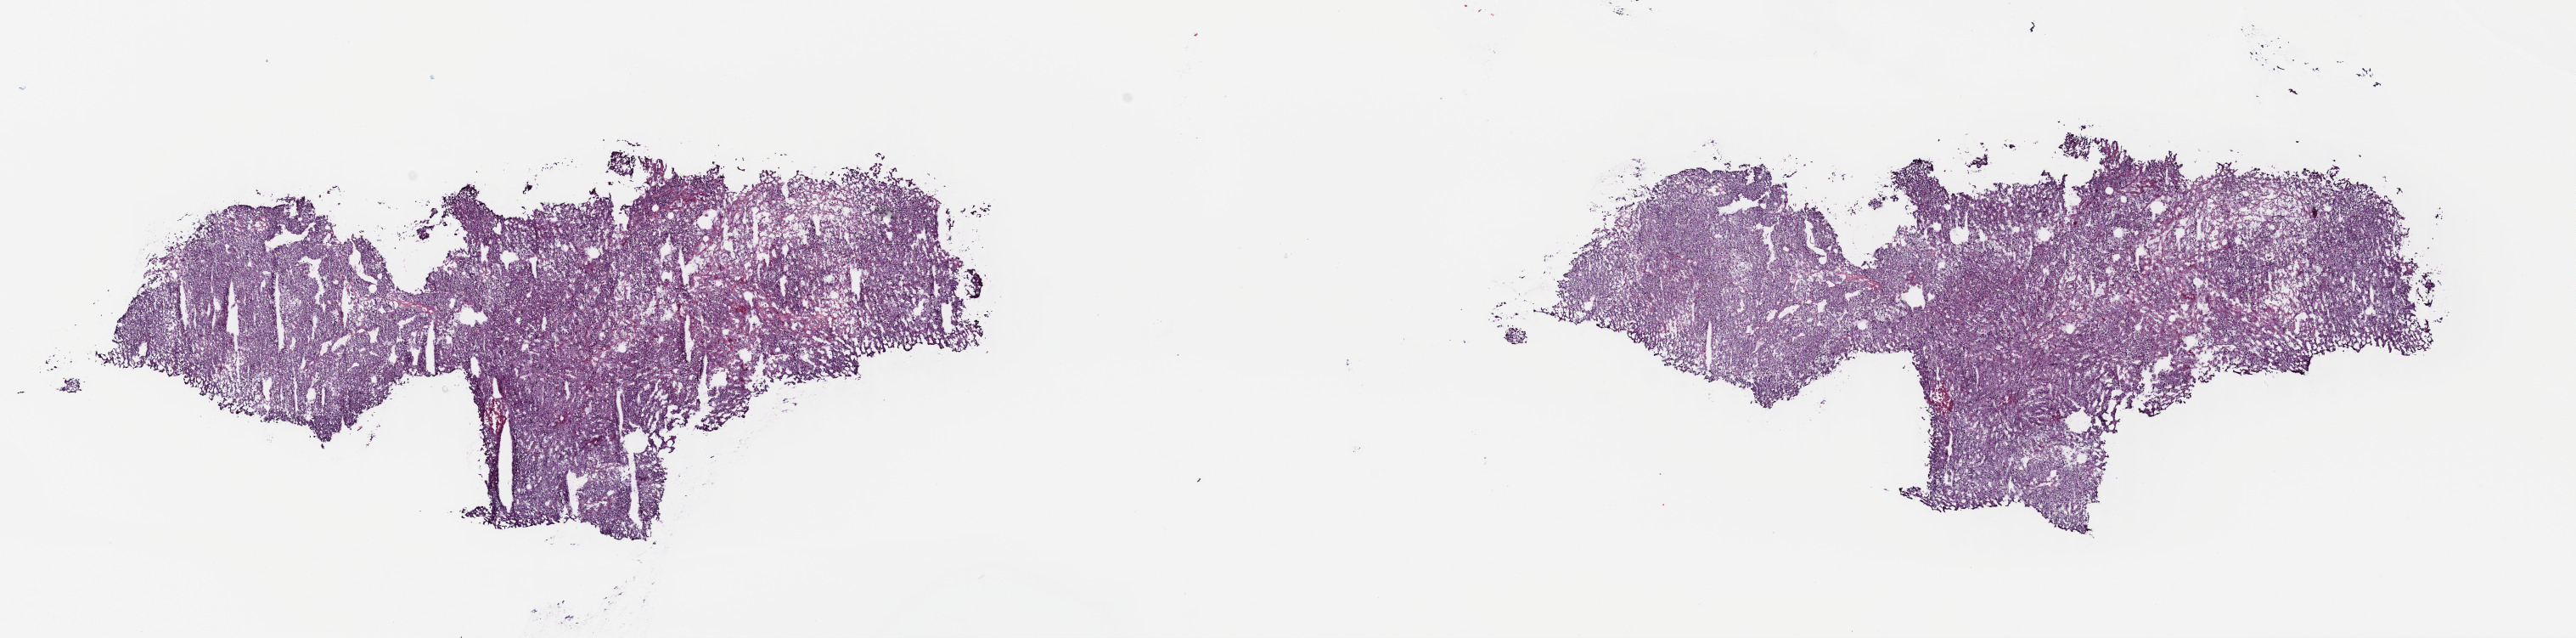
Whole-slide histology image, Hematoxylin and eosin (H&E) stained — whole scanned area (about 23.8 x 5.9 mm) shown as a low-resolution overview; frozen section from the top of the tissue portion; sample: primary tumour, adrenal cortex. Female, age 17 years at initial diagnosis.
Diagnosis: Adrenal cortical carcinoma (cortex of adrenal gland).